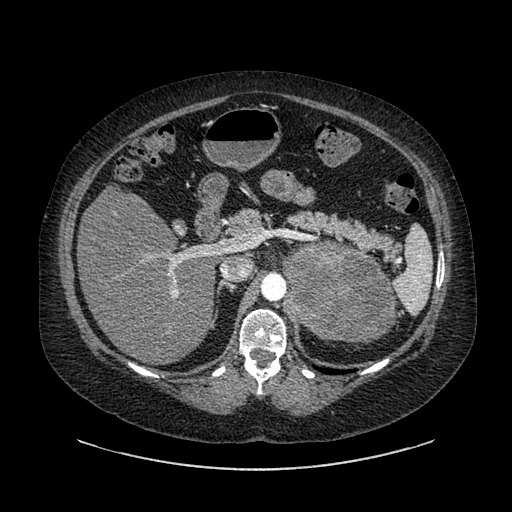
Contrast-enhanced abdominal CT, one axial slice. Reconstruction kernel SOFT. 120 kVp. Soft-tissue window (W 400 / L 40 HU). 512 × 512 image matrix, field of view 460 × 460 mm. Female patient, age 61 years. From the clinical record (not read from this slice): diagnosis: adrenocortical carcinoma; tumour side: left adrenal; tumour size at pathology: 13 cm; Ki-67 index: 79 %; stage (as recorded): 2.
Structures marked on this image (semi-automatically segmented with operator editing):
- mass: bounding box (x1, y1, x2, y2) in pixels: (284, 242, 393, 341)